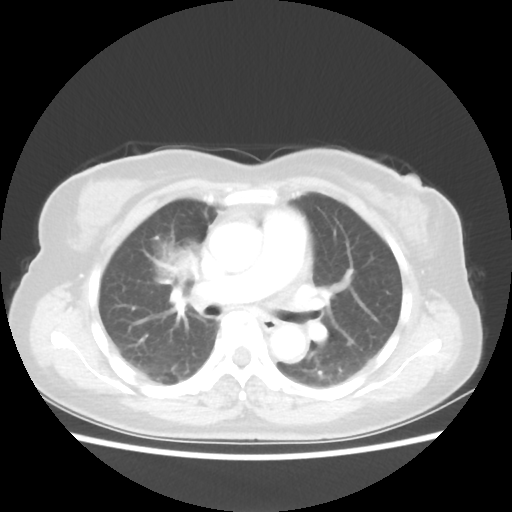
Chest CT, one axial slice. Slice 32 of 55 in the series (ordered by position). Reconstruction kernel STANDARD. 80 kVp. Lung window (W 1500 / L -600 HU). 512 × 512 image matrix, field of view 337 × 337 mm. Female patient, age 62 years. From the clinical record (not read from this slice): clinical TNM (as recorded): T4 N3 M0.
Structures marked on this image (rectangle marked by the reading radiologist):
- lung tumour (recorded histology: squamous cell carcinoma): box from (x=144, y=228) to (x=210, y=295) px